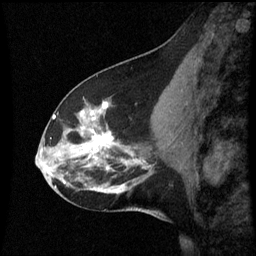
Breast MRI (dynamic contrast-enhanced), one sagittal slice. Dynamic contrast-enhanced series, image 2 of 3 at this slice position (ordered by acquisition). 1.5 T. TE 4.2 ms, TR 8.9 ms. 2 mm slice thickness. 256 × 256 image matrix, field of view 200 × 200 mm. Patient: female, 45 years. From the clinical record (not read from this slice): setting: breast cancer imaged before/during neoadjuvant chemotherapy; receptor status: HR-positive, HER2-negative.
Structures marked on this image (semi-automatically segmented with operator editing):
- analysis volume of interest (the breast-tissue region the enhancement analysis was run in; not a lesion): box from (x=46, y=94) to (x=171, y=205) px
- tumour enhancement mask (voxels above the 70 % enhancement threshold inside the analysis volume of interest): (x=54, y=102)–(x=137, y=163)